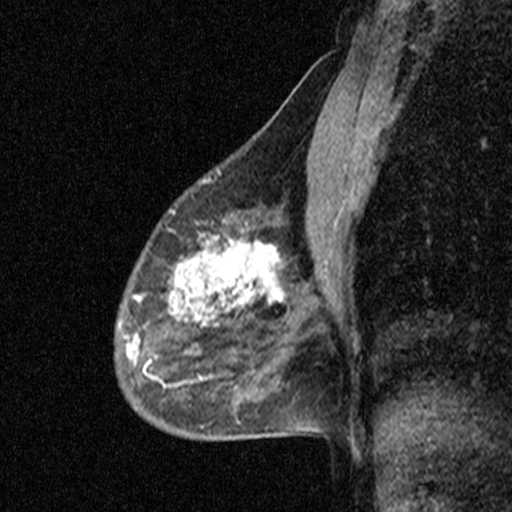
Breast MRI (dynamic contrast-enhanced), one sagittal slice. Position 28 of 44 along the scan axis. Dynamic contrast-enhanced study with each time point stored as its own series, time point 2 of 3 at this slice position (early post-contrast, ordered by acquisition time). 1.5 T. TE 4.5 ms, TR 11 ms. 3 mm slice thickness. 512 × 512 image matrix, field of view 200 × 200 mm. Female patient, age 53 years. From the clinical record (not read from this slice): setting: breast cancer imaged before/during neoadjuvant chemotherapy; receptor status: HR-positive, HER2-negative.
Annotated regions visible in this slice (semi-automatic segmentation, software-assisted and operator-edited):
- analysis volume of interest (the breast-tissue region the enhancement analysis was run in; not a lesion): bounding box [x1, y1, x2, y2] px = [88, 176, 313, 423]
- tumour enhancement mask (voxels above the 90 % enhancement threshold inside the analysis volume of interest): [128, 237, 283, 362]